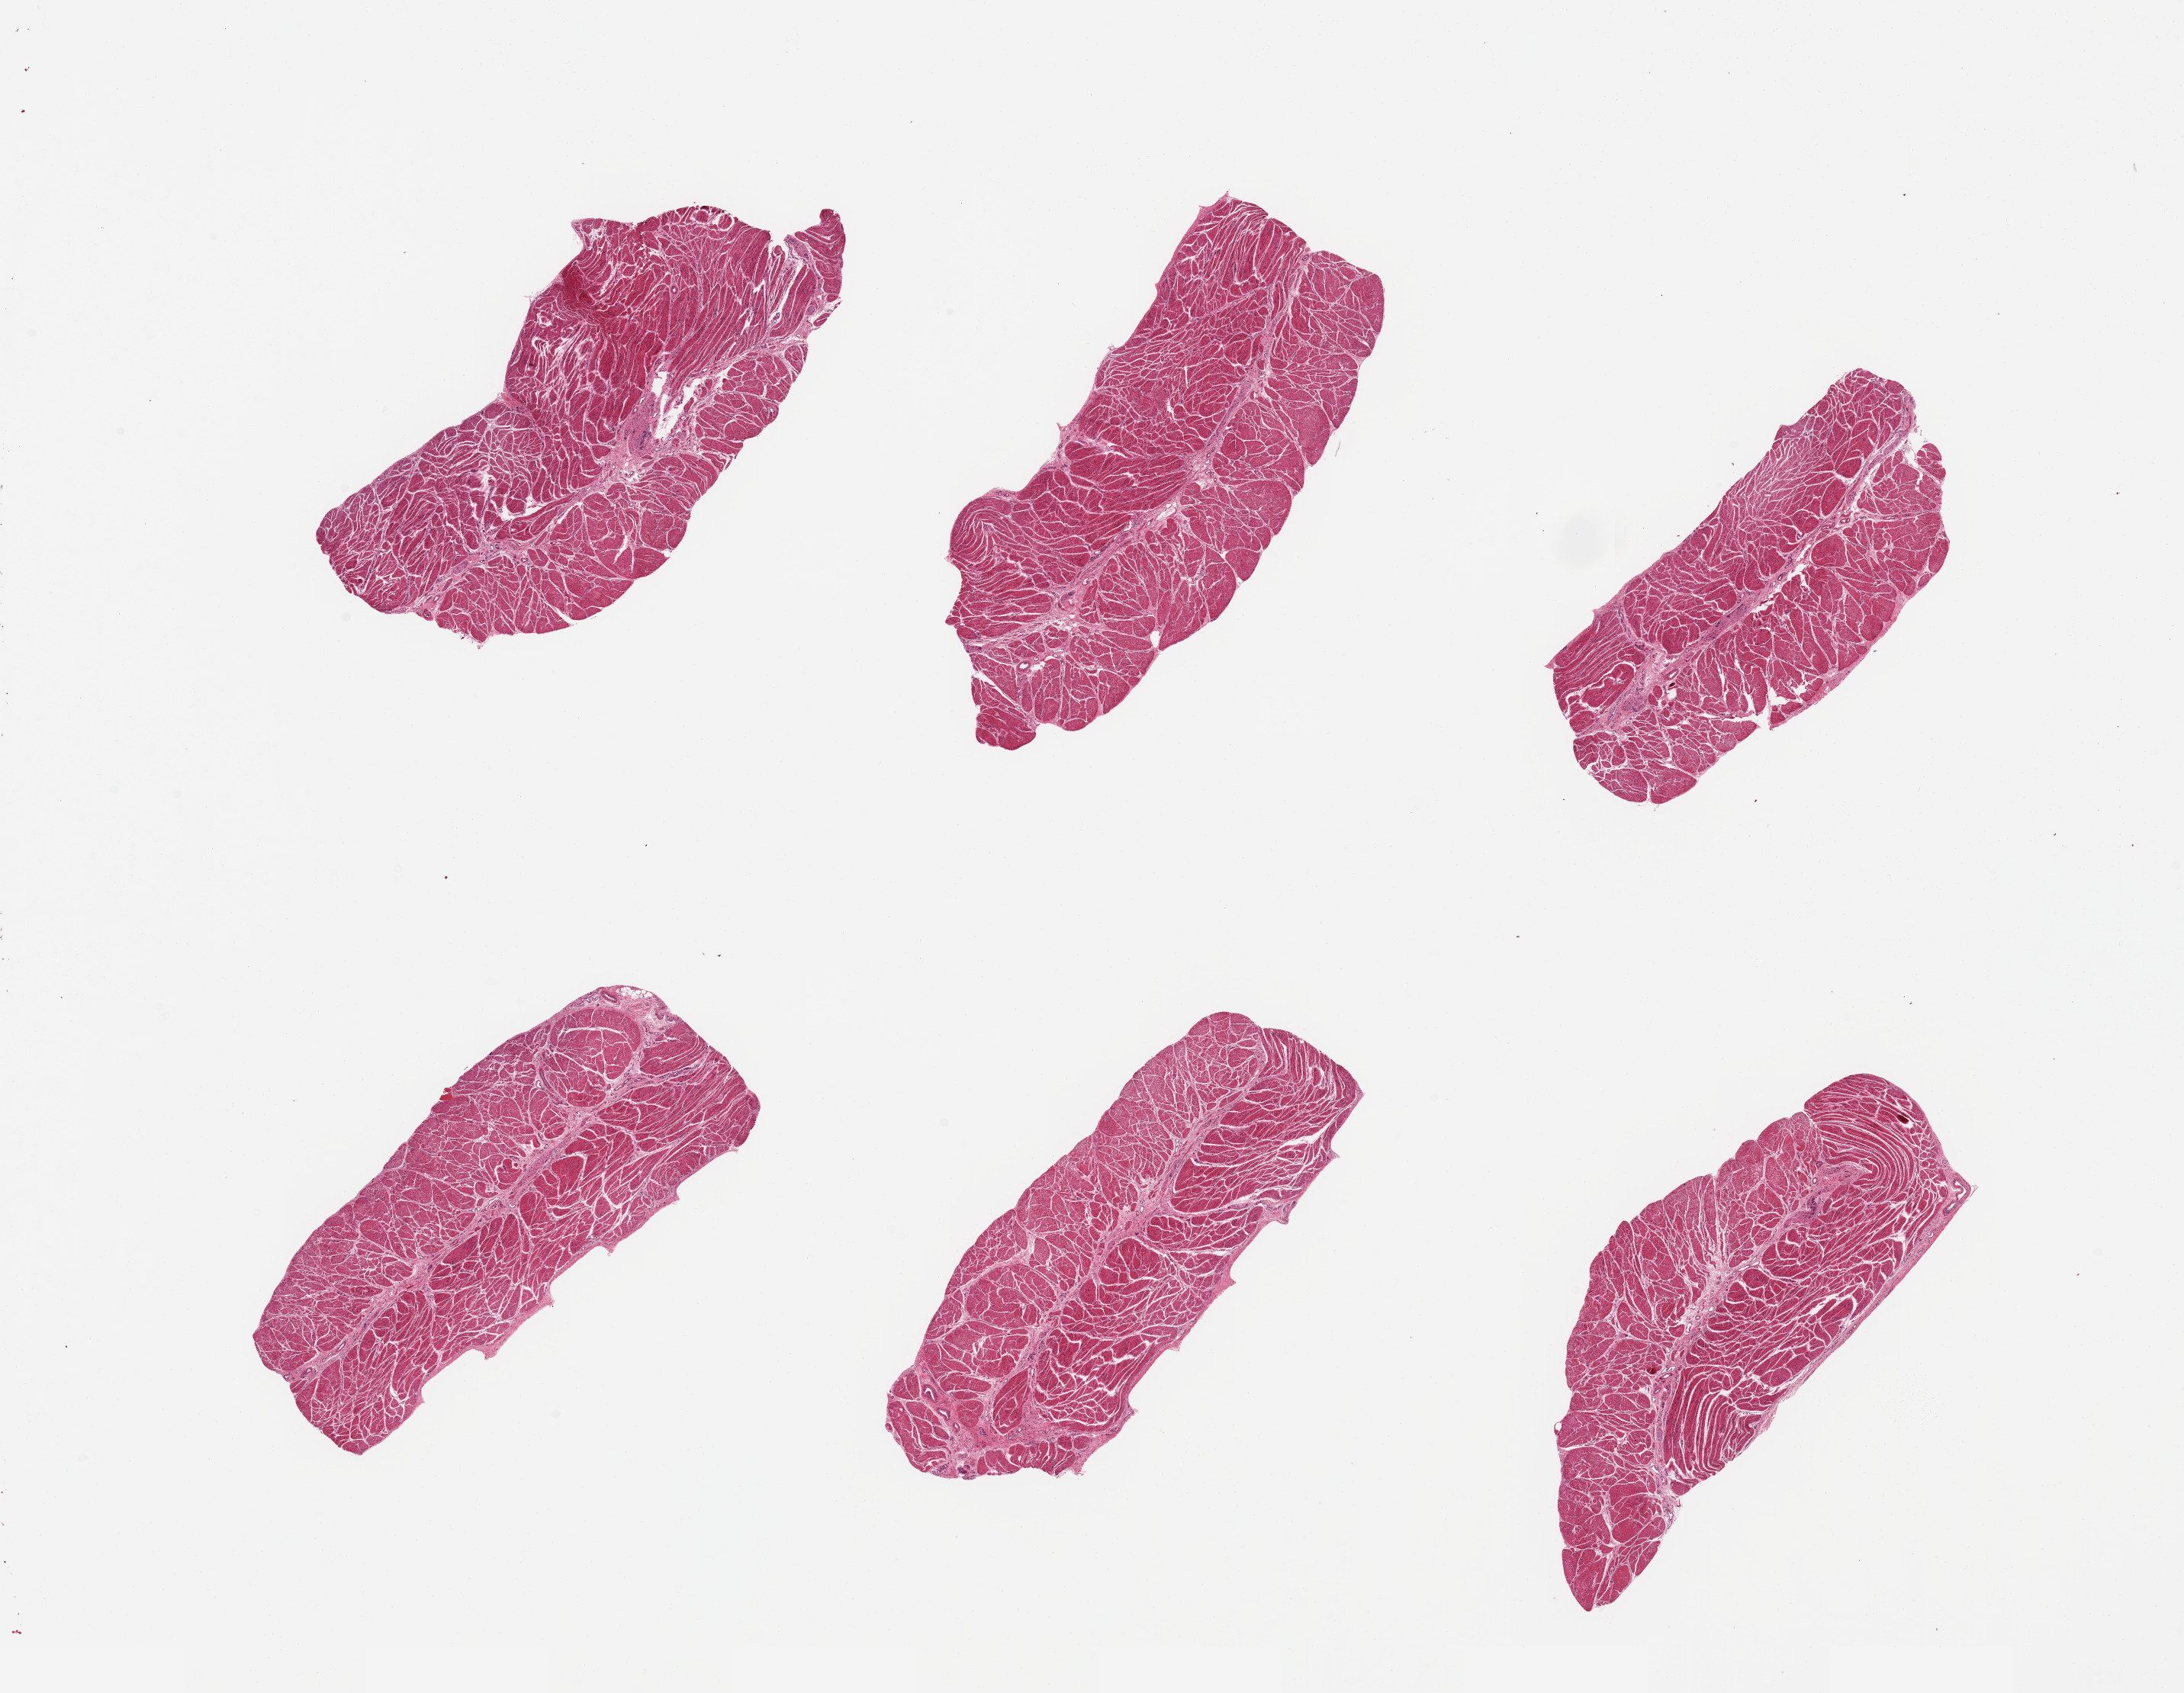
Digitized H&E-stained section, brightfield — low-resolution overview of the scanned area, about 22.6 x 17.6 mm; PAXgene-fixed paraffin-embedded (PFPE) section; section of esophageal muscle (target tissue); tissue donor sample. Male donor.
Pathologist's review note for this sample: 6 pieces; well trimmed target muscularis.